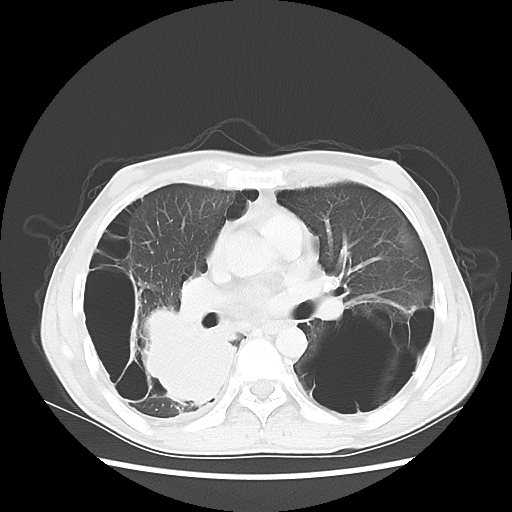
Chest CT, one axial slice; position 30 of 57 along the scan axis; reconstruction kernel LUNG; lung window (W 1500 / L -600 HU); 5 mm slice thickness; 512 × 512 image matrix, field of view 351 × 351 mm. Patient: male, 41 years. Case-level facts recorded for this patient, not image findings: clinical TNM (as recorded): T4 N0 M1a; histopathological grade: G3.
Annotated regions visible in this slice (rectangle marked by the reading radiologist):
- lung tumour (recorded histology: large cell carcinoma): box from (x=129, y=300) to (x=254, y=424) px